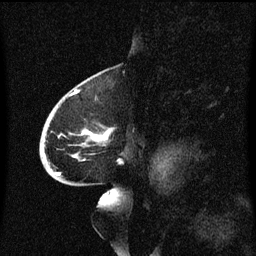
Breast MRI (dynamic contrast-enhanced), one sagittal slice. Position 38 of 60 along the scan axis. Dynamic contrast-enhanced series, image 2 of 3 at this slice position (ordered by acquisition). 1.5 T. TE 4.2 ms, TR 8.4 ms. 2 mm slice thickness. 256 × 256 image matrix, field of view 200 × 200 mm. Patient: female, 68 years. From the clinical record (not read from this slice): setting: breast cancer imaged before/during neoadjuvant chemotherapy; receptor status: triple-negative.
Structures marked on this image (semi-automatic segmentation, software-assisted and operator-edited):
- analysis volume of interest (the breast-tissue region the enhancement analysis was run in; not a lesion): bounding box [x1, y1, x2, y2] px = [41, 94, 124, 173]
- tumour enhancement mask (voxels above the 70 % enhancement threshold inside the analysis volume of interest): [44, 130, 112, 159]